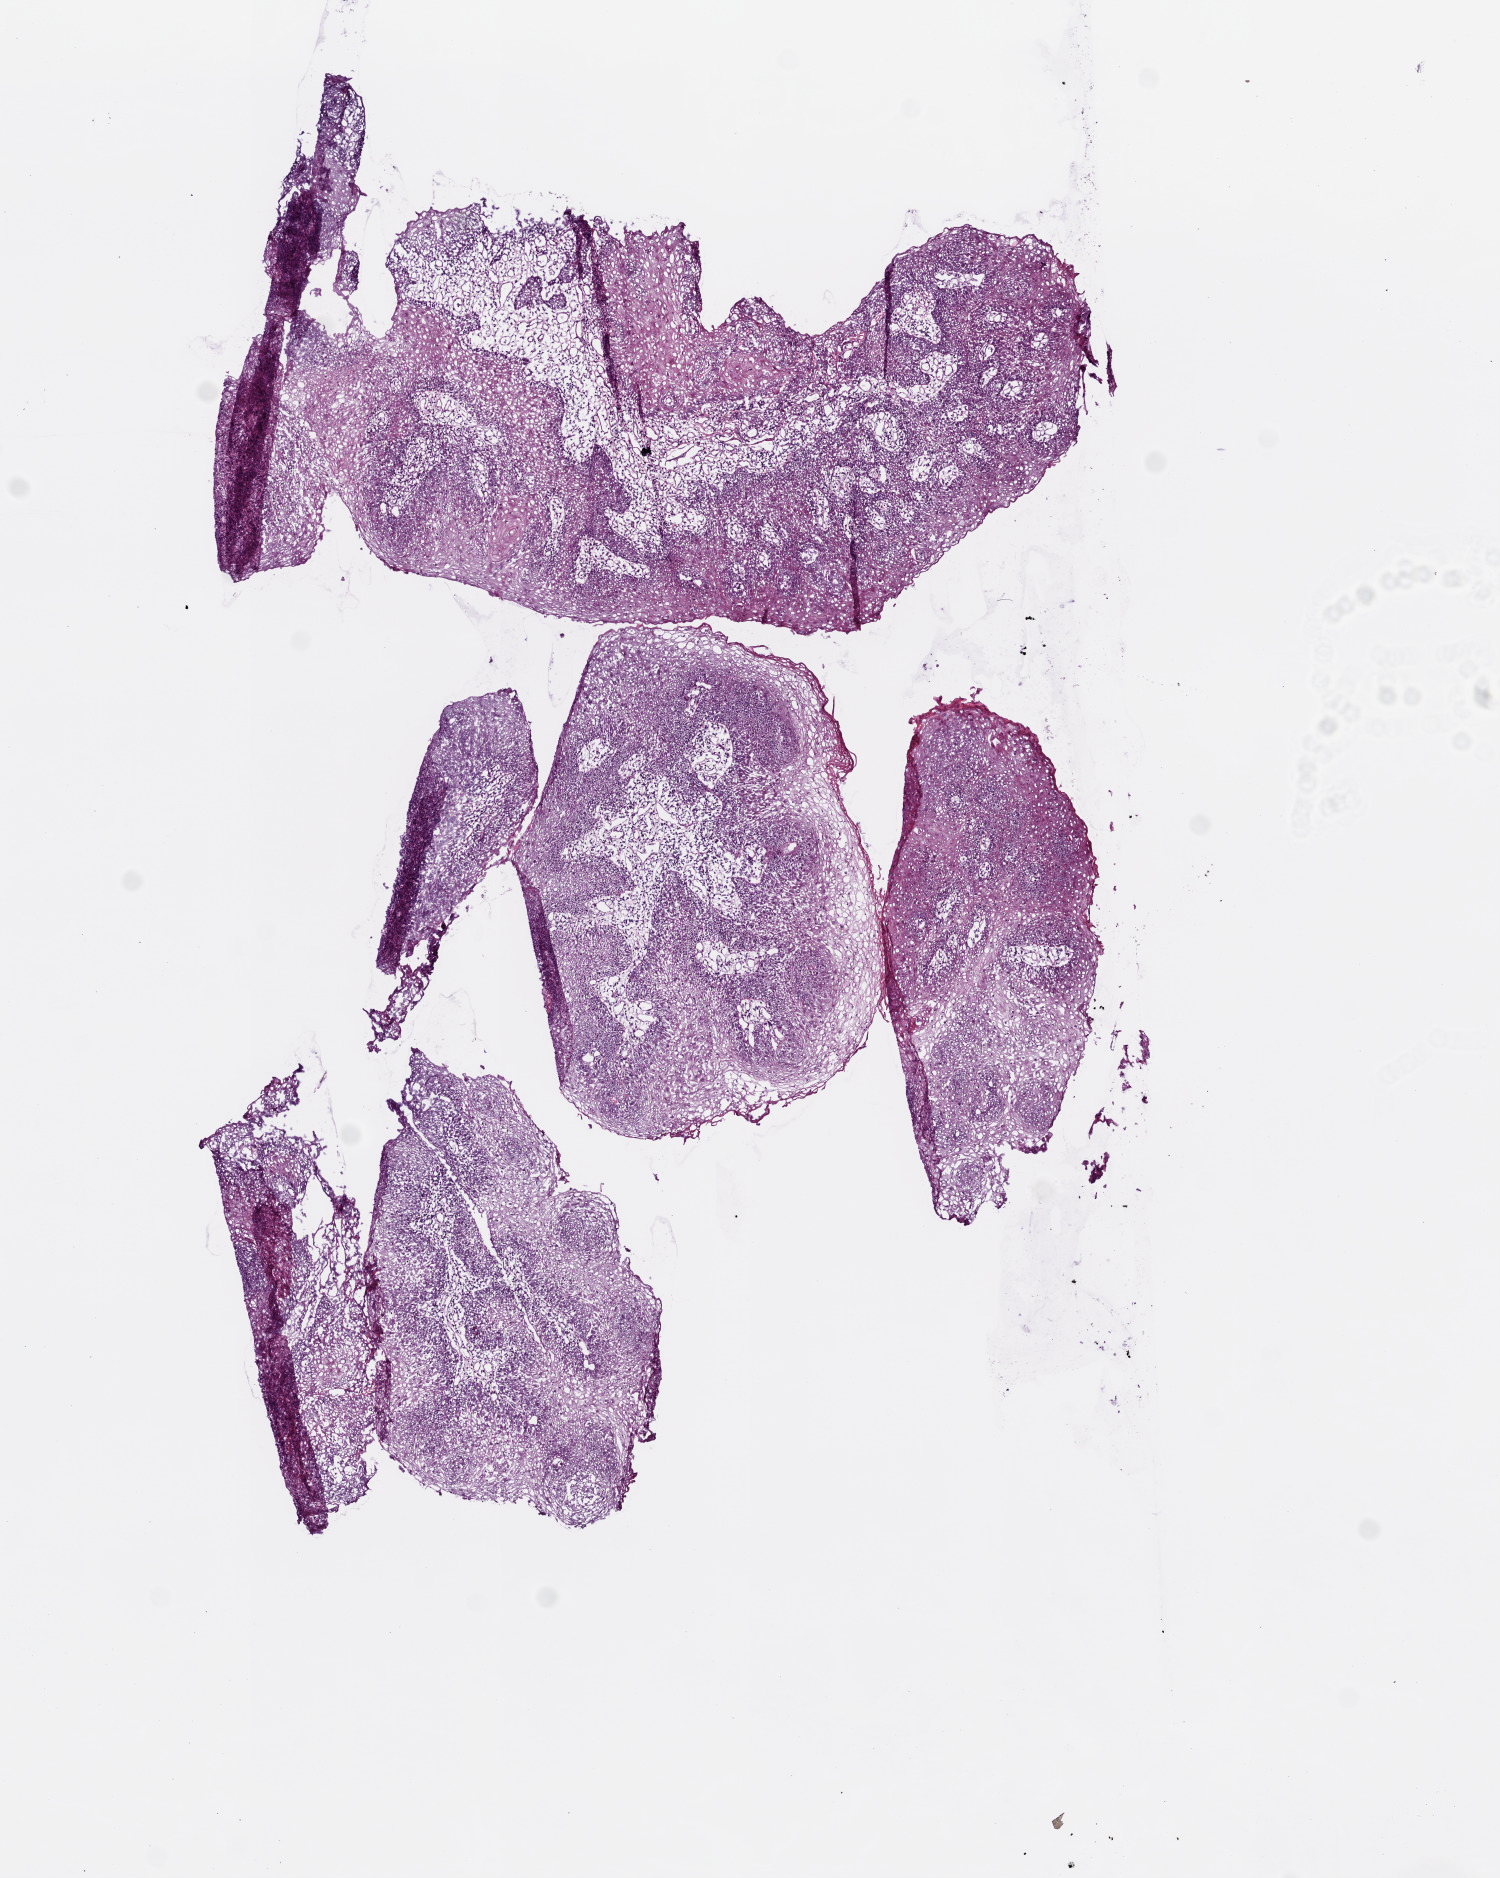
Whole-slide histology image, H&E, low-resolution overview of the scanned area, about 6.0 x 7.5 mm (slide scanned at 20x); frozen section; primary tumour sample from the head and neck. Female, age 58 years at initial diagnosis. Histologic grade: G3 (poorly differentiated). Slide review estimates, as recorded: tumour cells 85%, tumour nuclei 80%, normal cells 0%, stromal cells 15%, necrosis 0%.
AJCC pathologic stage: II. Histologic diagnosis: Squamous cell carcinoma, NOS (floor of mouth, NOS). Lymph nodes positive (case pathology): 0 of 81 examined.